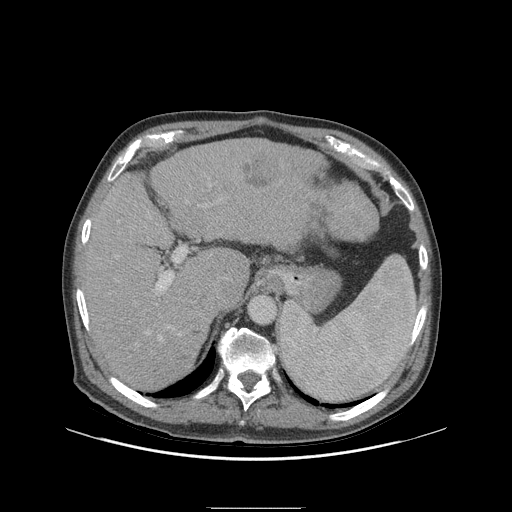
Contrast-enhanced abdominal CT (liver protocol), one axial slice; position 67 of 105 along the scan axis; soft-tissue window (W 400 / L 40 HU); 2.5 mm slice thickness; 512 × 512 image matrix, field of view 440 × 440 mm. Case-level facts recorded for this patient, not image findings: diagnosis: hepatocellular carcinoma (patient treated with transarterial chemoembolisation; whether this scan precedes or follows treatment is not stated here); TNM stage (as recorded): Stage-I; Child-Pugh class: A.
Annotated regions visible in this slice (semi-automatically segmented with operator editing):
- liver parenchyma outside the tumour (the mass and vessels are separate outlines, so this box may not span the whole liver): bounding box [x1, y1, x2, y2] px = [80, 138, 374, 390]
- mass: [243, 157, 277, 187]
- liver vessels: [156, 272, 174, 340]